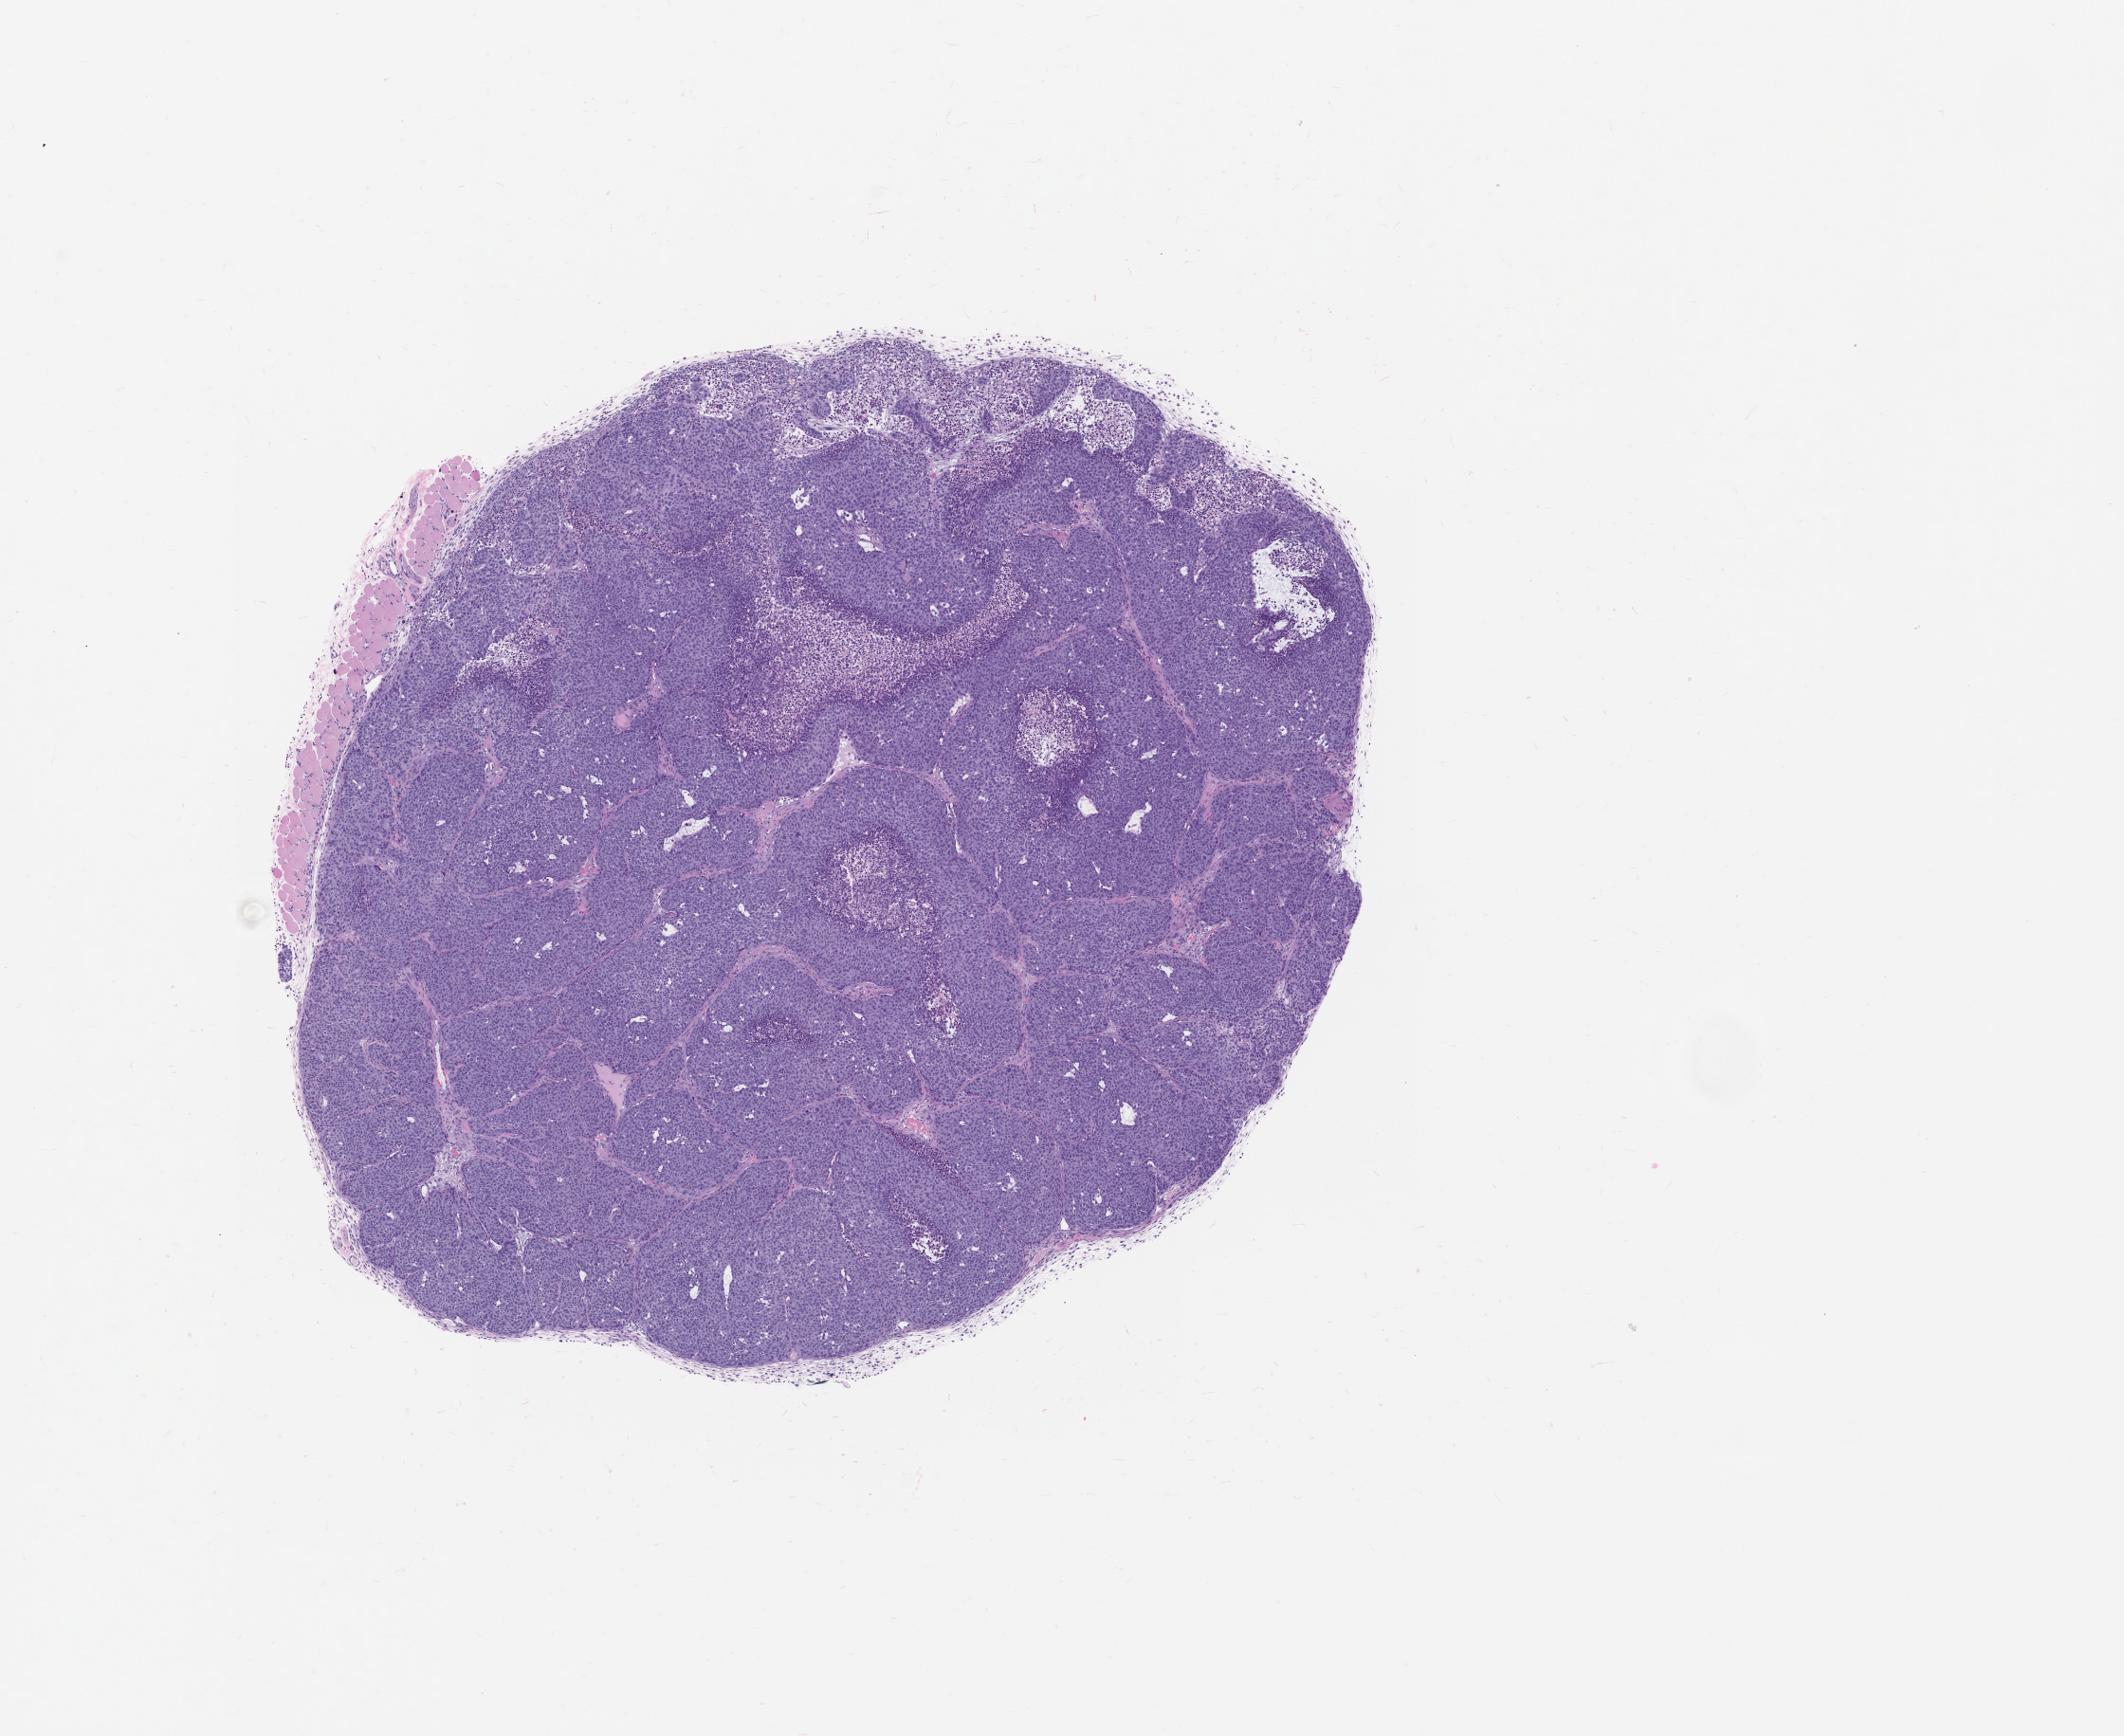
Whole-slide image, haematoxylin and eosin: patient-derived xenograft (human tumor grown in a mouse), passage 1 — a low-resolution overview of the entire scanned area, about 9.0 x 7.3 mm, formalin-fixed paraffin-embedded section, tumor site category: head and neck.
Originating patient diagnosis: Head and Neck Squamous Cell Carcinoma.